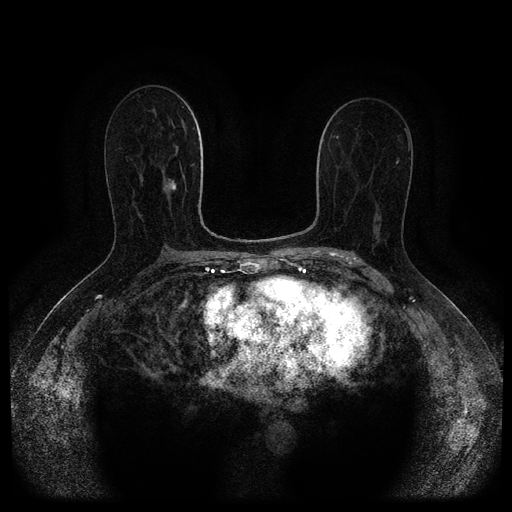
Breast MRI (dynamic contrast-enhanced, multi-phase), one axial slice; position 57 of 116 along the scan axis; dynamic contrast-enhanced series, time point 2 of 5 at this slice position (early post-contrast); 1.5 T; TE 2.7 ms, TR 5.4 ms; 512 × 512 image matrix, field of view 340 × 340 mm. Patient: female, 71 years.
Annotated regions visible in this slice (semi-automatic segmentation, software-assisted and operator-edited):
- breast lesion (labelled 'tumour' in the annotation; benign lesions carry a separate 'benign' label): box from (x=164, y=180) to (x=176, y=191) px